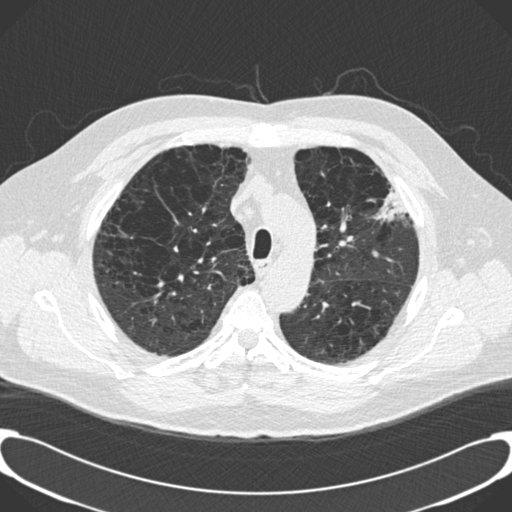
Low-dose screening chest CT, one axial slice; slice 149 of 189 in the series (ordered by position); lung window (W 1500 / L -600 HU); 2 mm slice thickness; 512 × 512 image matrix, field of view 380 × 380 mm.
Annotated regions visible in this slice (outlined manually by an expert reader):
- lesion 1 (tumor, upper lobe of left lung): bounding box (x1, y1, x2, y2) in pixels: (374, 187, 408, 221)